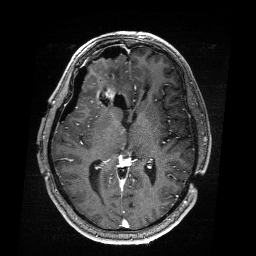
Brain MRI from a brain-tumour surgery series, one axial slice. T1-weighted post-contrast. 1 mm slice thickness. 256 × 256 image matrix. Case-level facts recorded for this patient, not image findings: histopathology: Astrocytoma; WHO grade: 4; IDH mutation: yes; tumour location: Right Frontal.
Outlined on this slice (outlined manually by an expert reader):
- residual tumour: bounding box [x1, y1, x2, y2] px = [92, 83, 116, 99]